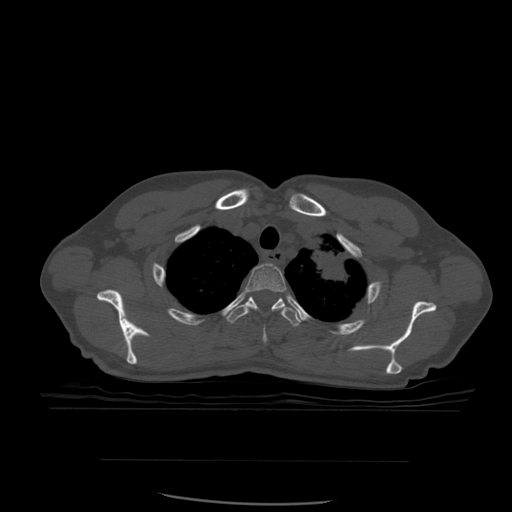
CT including the spine, one axial slice; position 449 of 574 along the scan axis; bone window (W 1800 / L 400 HU); 1.25 mm slice thickness; 512 × 512 image matrix. Patient age 48 years. Case-level facts recorded for this patient, not image findings: primary cancer: lung; vertebrae with lytic lesions (as recorded): T11.
Structures marked on this image (semi-automatically segmented with operator editing):
- T2 vertebra: bounding box (x1, y1, x2, y2) in pixels: (246, 263, 287, 343)
- T3 vertebra: (227, 297, 302, 327)